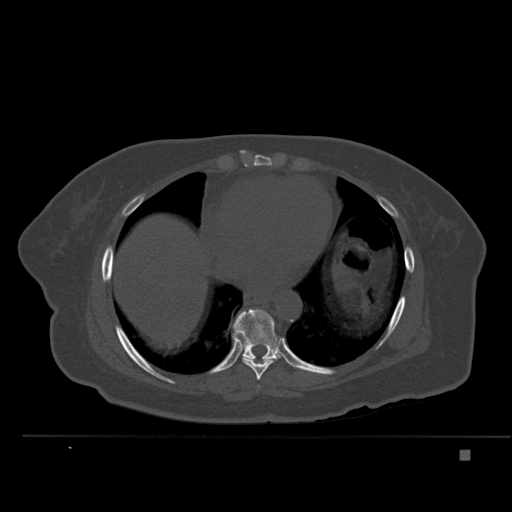
CT including the spine, one axial slice; position 305 of 477 along the scan axis; bone window (W 1800 / L 400 HU); 1.5 mm slice thickness; 512 × 512 image matrix. Female patient, age 74 years. Case-level facts recorded for this patient, not image findings: primary cancer: colon.
Structures marked on this image (semi-automatic segmentation, software-assisted and operator-edited):
- T8 vertebra: bounding box <243,358,274,380> (left, top, right, bottom; pixels)
- T9 vertebra: <233,309,280,362>